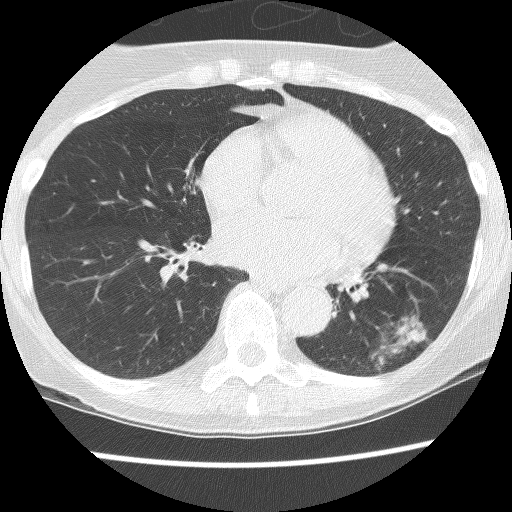
Low-dose screening chest CT, axial slice, third screening round (two years after baseline), lung window (W 1500 / L -600 HU), 2.5 mm slice thickness. Female, age 61 years at enrolment. Current smoker at enrolment.
- Expert reader's lesion annotation, bounding box (x1, y1, x2, y2) in pixels: (328, 288, 451, 391).
- The screening reader recorded 2 non-calcified nodules or masses ≥4 mm on this exam (left lower lobe, left lower lobe); which of them this box marks is not recorded.
- Later outcome: lung cancer diagnosed 166 days after this screen — non-small cell carcinoma, left lower lobe, poorly differentiated (G3), stage IB (AJCC 6th edition), 100 mm at pathology.